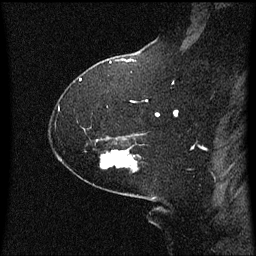
Breast MRI (dynamic contrast-enhanced), one sagittal slice. Dynamic contrast-enhanced series, image 2 of 3 at this slice position (ordered by acquisition). 1.5 T. TE 4.2 ms, TR 8 ms. 2.1 mm slice thickness. 256 × 256 image matrix, field of view 200 × 200 mm. Patient: female, 59 years.
Structures marked on this image (semi-automatically segmented with operator editing):
- analysis volume of interest (the breast-tissue region the enhancement analysis was run in; not a lesion): bounding box [x1, y1, x2, y2] px = [86, 148, 141, 173]
- tumour enhancement mask (voxels above the 70 % enhancement threshold inside the analysis volume of interest): [134, 162, 137, 165]